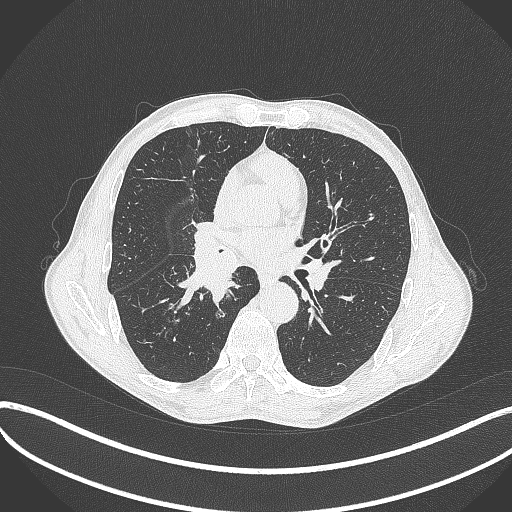
Chest CT, one axial slice; slice 228 of 481 in the series (ordered by position); reconstruction kernel B70f; 120 kVp; lung window (W 1500 / L -600 HU); 1 mm slice thickness; 512 × 512 image matrix, field of view 400 × 400 mm. Male patient, age 65 years. Case-level facts recorded for this patient, not image findings: clinical TNM (as recorded): T2a N0 M0; histopathological grade: G2.
Structures marked on this image (bounding box drawn by a radiologist):
- lung tumour (recorded histology: squamous cell carcinoma): bounding box <179,229,238,311> (left, top, right, bottom; pixels)